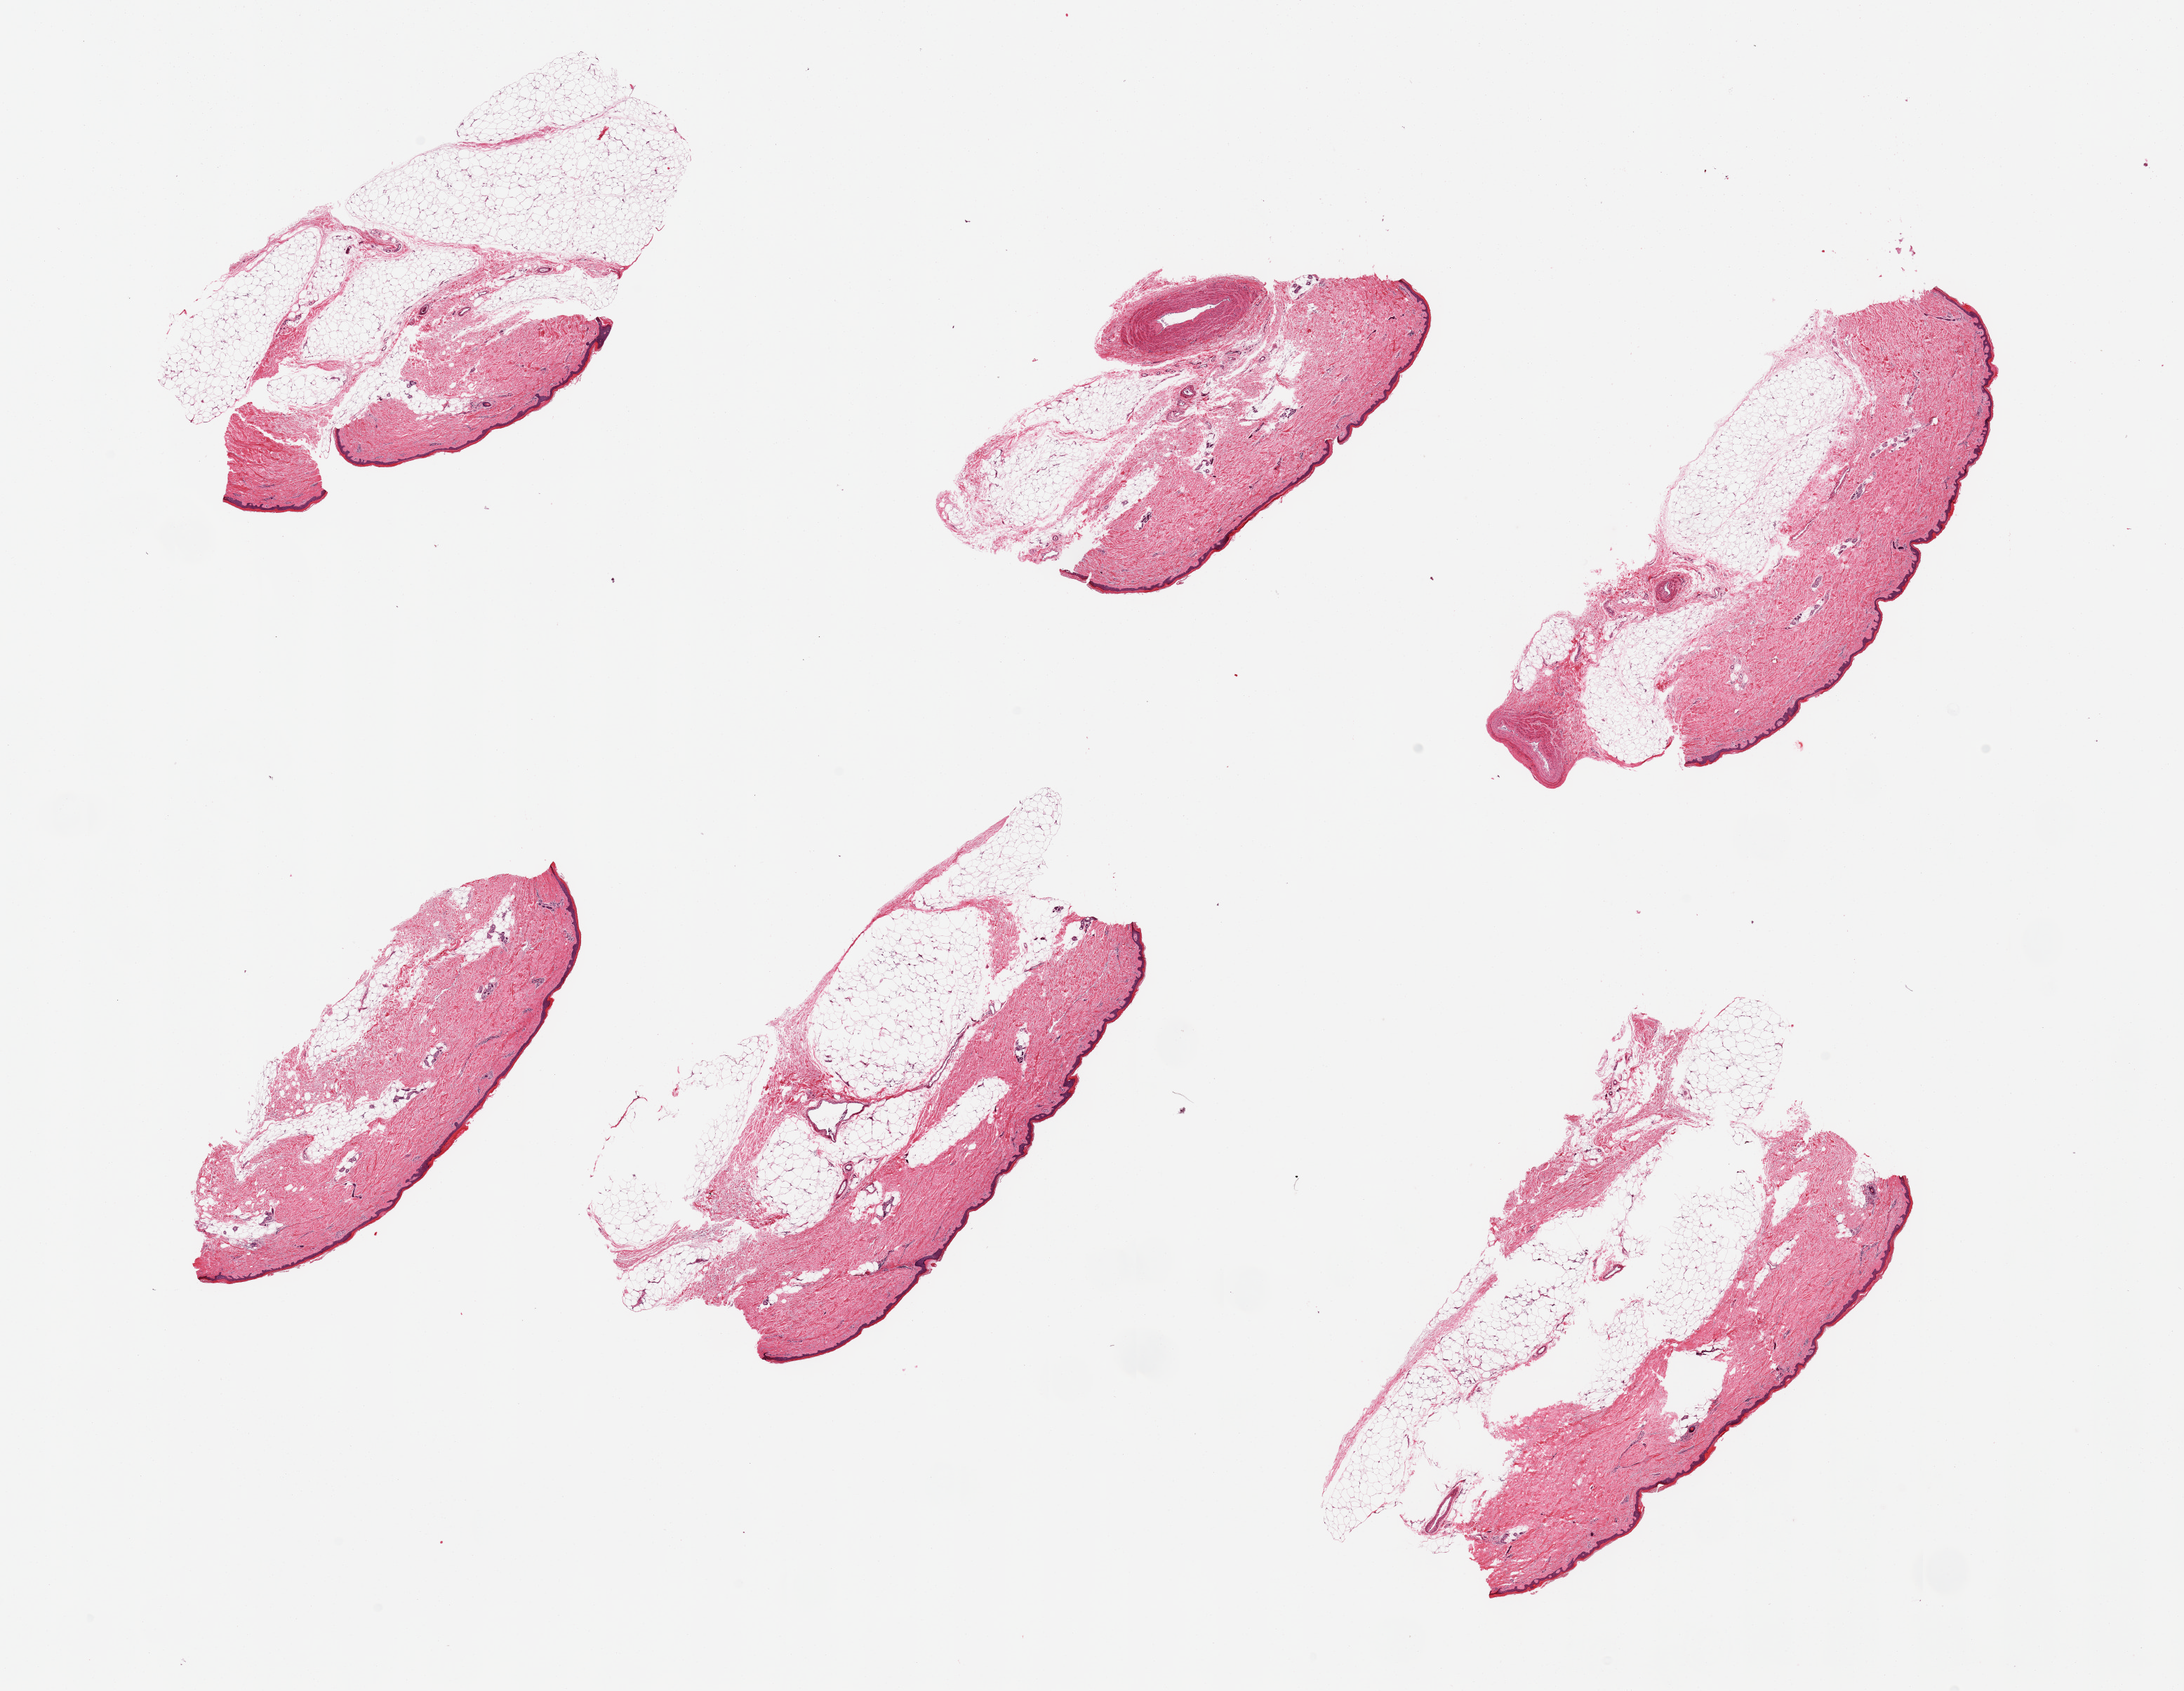
Haematoxylin and eosin whole-slide image, brightfield, shown as a low-resolution overview of the whole scanned area (about 24.6 x 19.1 mm), PAXgene-fixed, paraffin-embedded tissue, sampled site (target tissue): skin of lower leg, donor tissue sample. Donor: female.
Pathologist's review note for this sample: 6 pieces; excessive subcutaneous fat up to 1.7mm thick.